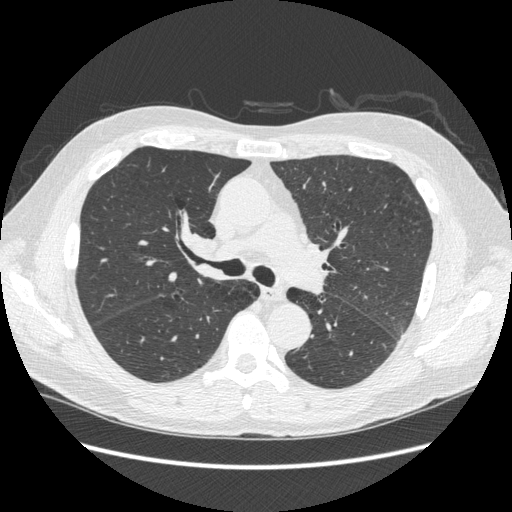
Low-dose screening chest CT, axial slice; third annual screen; lung window (W 1500 / L -600 HU); 1.25 mm slice thickness; standard (soft-tissue) reconstruction kernel (STANDARD); slice 104 of 258 in the series; 512 × 512 image matrix, field of view 380 × 380 mm. Male, age 59 years at enrolment.
- Lesion marked by an expert reader, box from (x=177, y=225) to (x=227, y=269) px.
- The screening reader recorded 2 non-calcified nodules or masses ≥4 mm on this exam (right upper lobe, left lower lobe); which of them this box marks is not recorded.
- Official screen result: negative screen, minor abnormalities not suspicious for lung cancer.
- Later outcome: lung cancer diagnosed 169 days after this screen — squamous cell carcinoma, keratinizing, NOS, right hilum, stage IIIB (AJCC 6th edition).